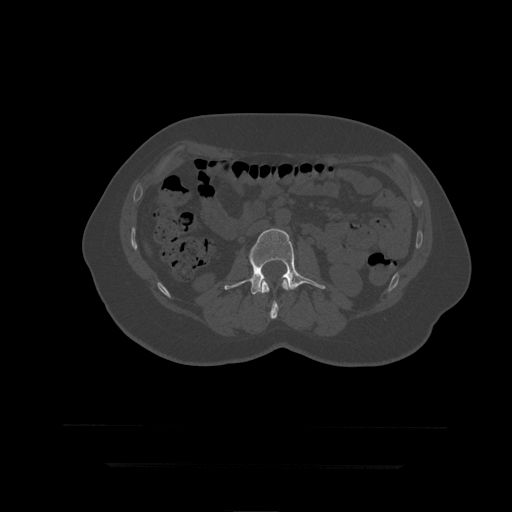
CT including the spine, one axial slice; position 131 of 399 along the scan axis; bone window (W 1800 / L 400 HU); 512 × 512 image matrix, field of view 450 × 450 mm. Patient age 41 years. From the clinical record (not read from this slice): primary cancer: breast.
Annotated regions visible in this slice (semi-automatically segmented with operator editing):
- L2 vertebra: bounding box <261,278,289,319> (left, top, right, bottom; pixels)
- L3 vertebra: <225,229,326,295>